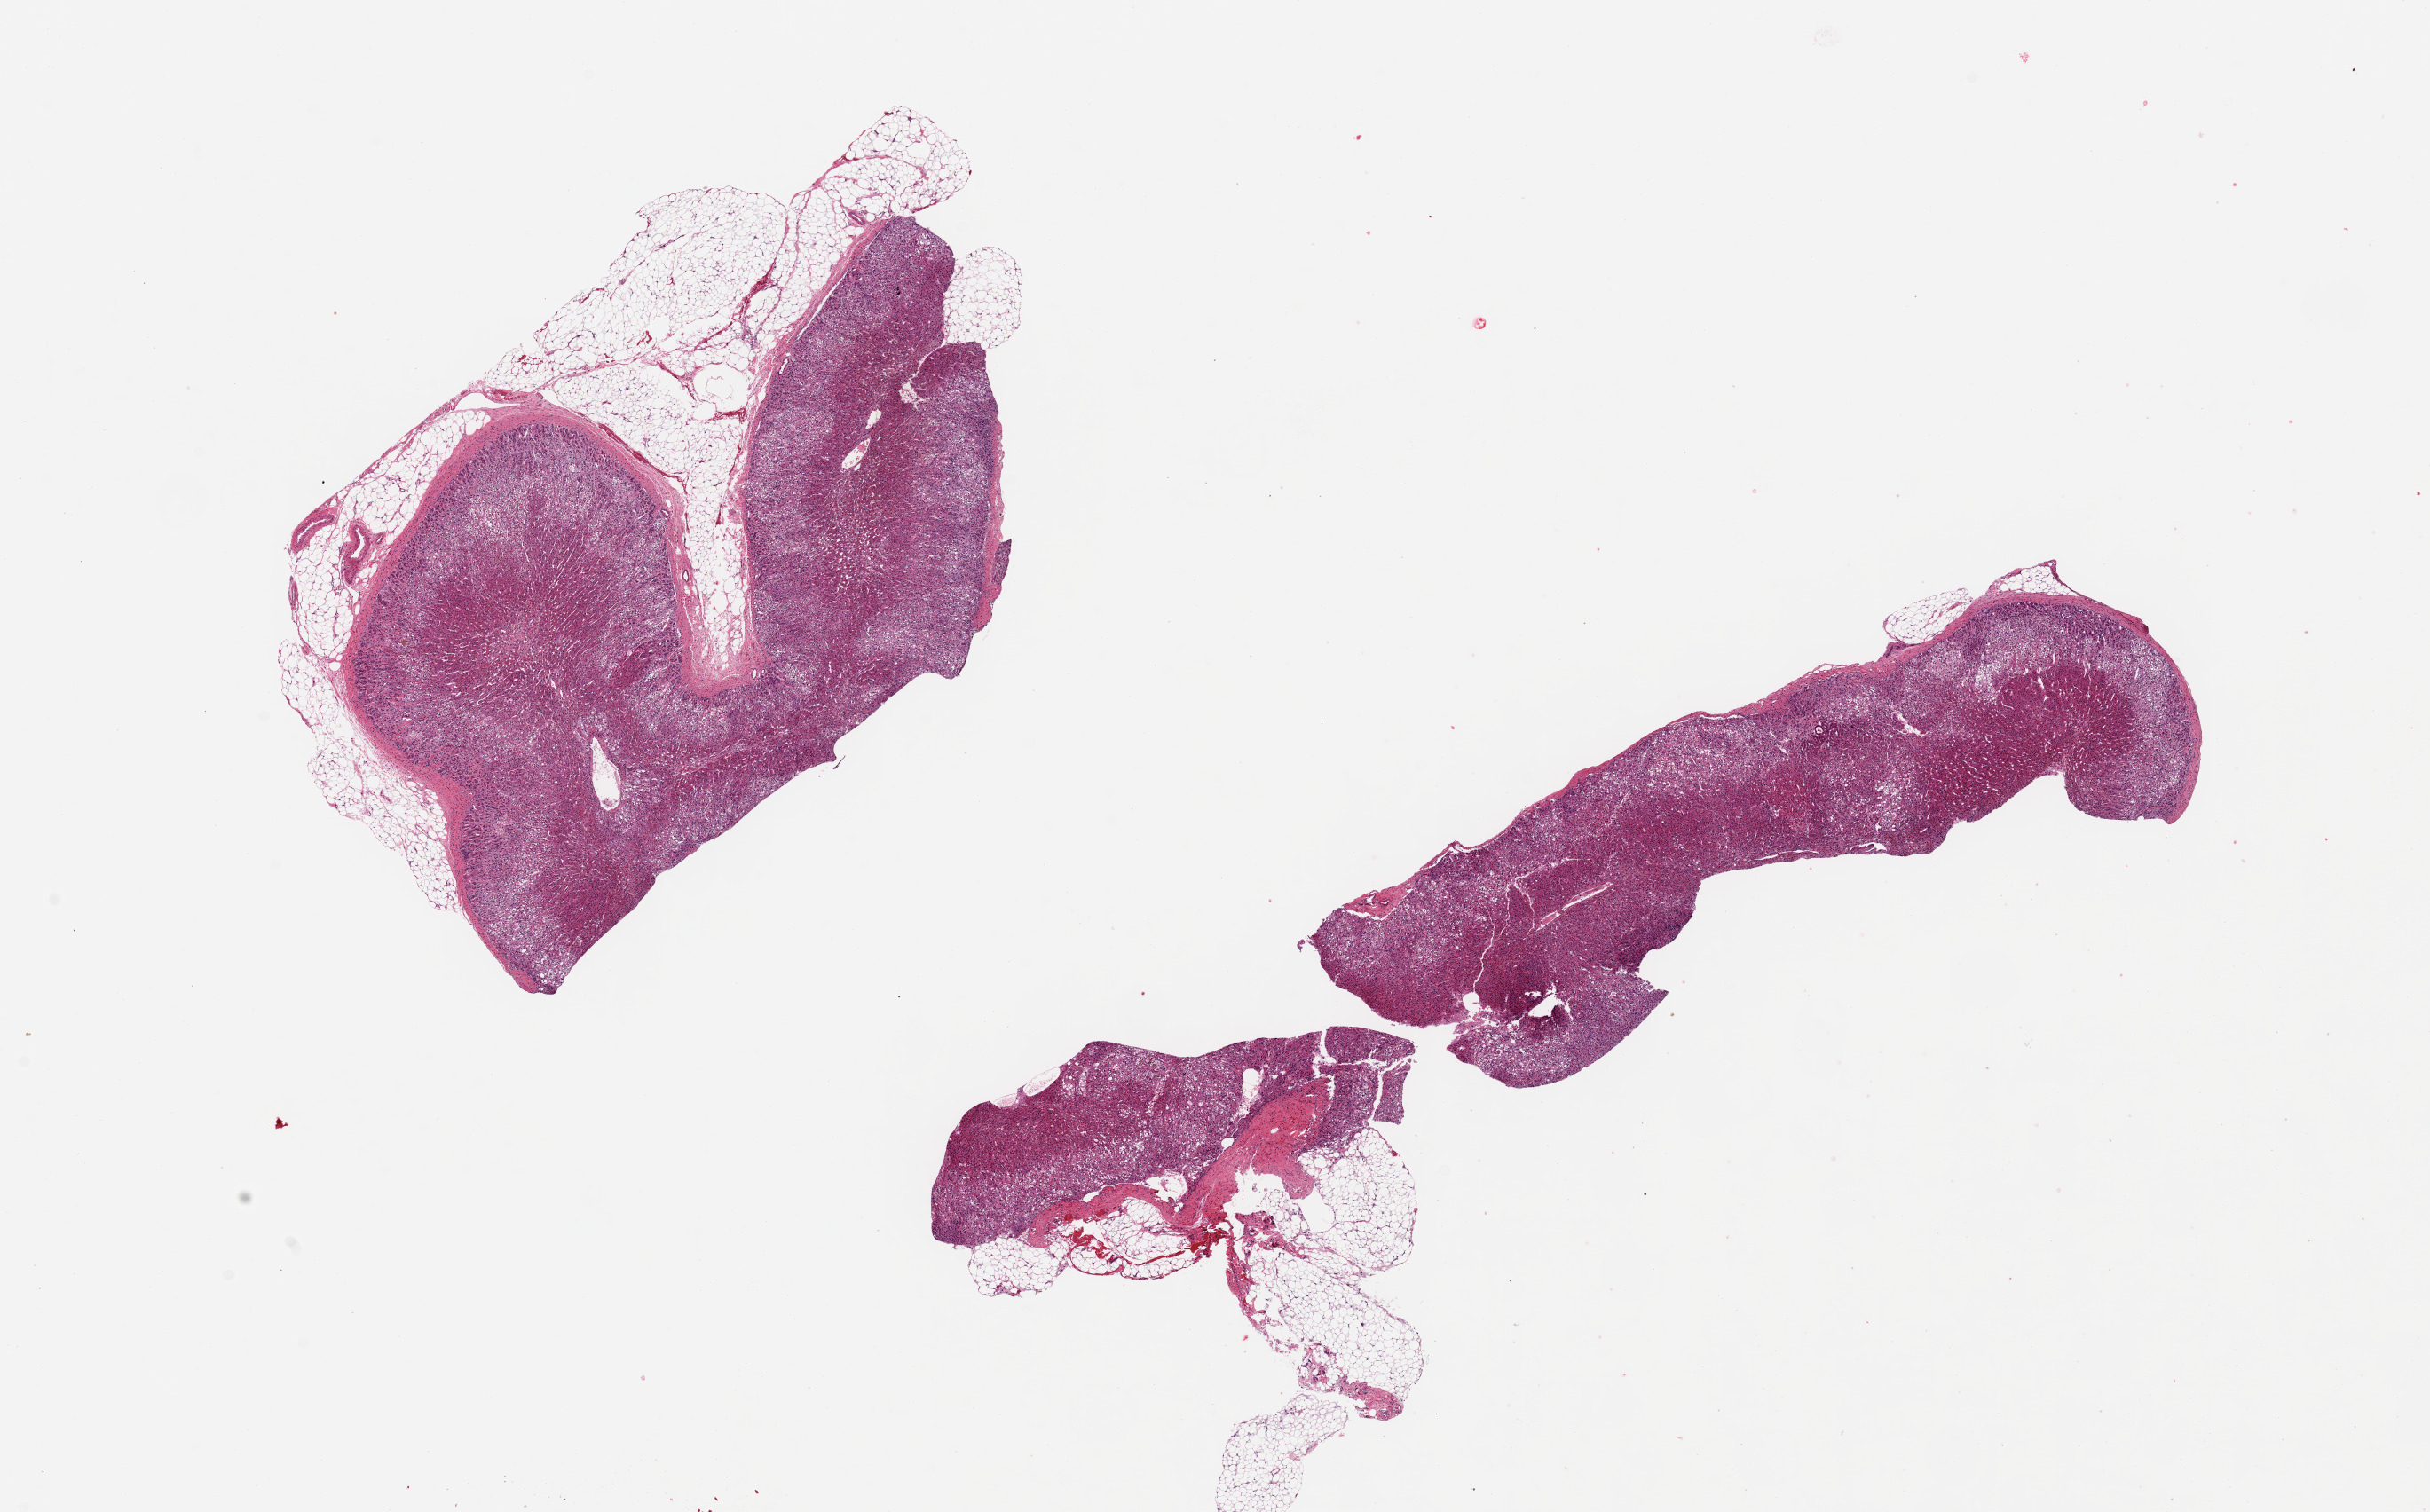
Hematoxylin and eosin (H&E) whole-slide image — low-resolution overview of the scanned area, about 21.7 x 13.5 mm (acquisition: 20x scan). PAXgene-fixed, paraffin-embedded tissue. Sampled site (target tissue): adrenal gland. Donor tissue sample. Donor sex: female.
Reviewer comment on this tissue sample: 2 aliquots, ~ 9x3.5mm, cortex only, well preserved. One aliquot ~30% adherent fat on one edge.